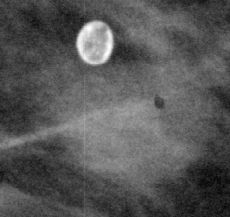
Cropped region of a digitized screen-film mammogram centred on a radiologist-marked abnormality, left breast, MLO view.
- Marked abnormality: mass, shape oval, margins microlobulated; BI-RADS assessment category 4; pathology (as recorded): malignant.